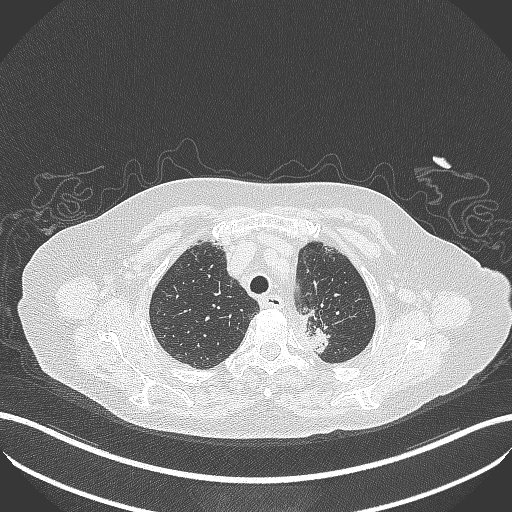
Chest CT, one axial slice. Slice 279 of 353 in the series (ordered by position). 100 kVp. Lung window (W 1500 / L -600 HU). 1 mm slice thickness. 512 × 512 image matrix, field of view 400 × 400 mm. Patient: female, 81 years. Case-level facts recorded for this patient, not image findings: clinical TNM (as recorded): T2a N0 M0.
Outlined on this slice (rectangle marked by the reading radiologist):
- lung tumour (recorded histology: adenocarcinoma): bounding box [x1, y1, x2, y2] px = [297, 300, 332, 357]